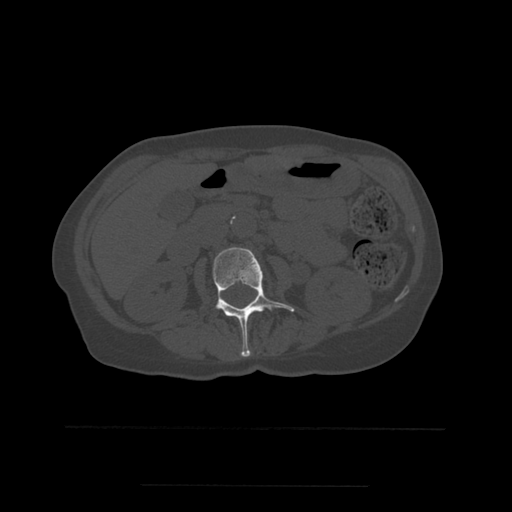
CT including the spine, one axial slice. Slice 211 of 544 in the series (ordered by position). Bone window (W 1800 / L 400 HU). 1.25 mm slice thickness. 512 × 512 image matrix. Patient age 58 years. From the clinical record (not read from this slice): primary cancer: lung.
Structures marked on this image (semi-automatic segmentation, software-assisted and operator-edited):
- L2 vertebra: bounding box <213,247,295,357> (left, top, right, bottom; pixels)